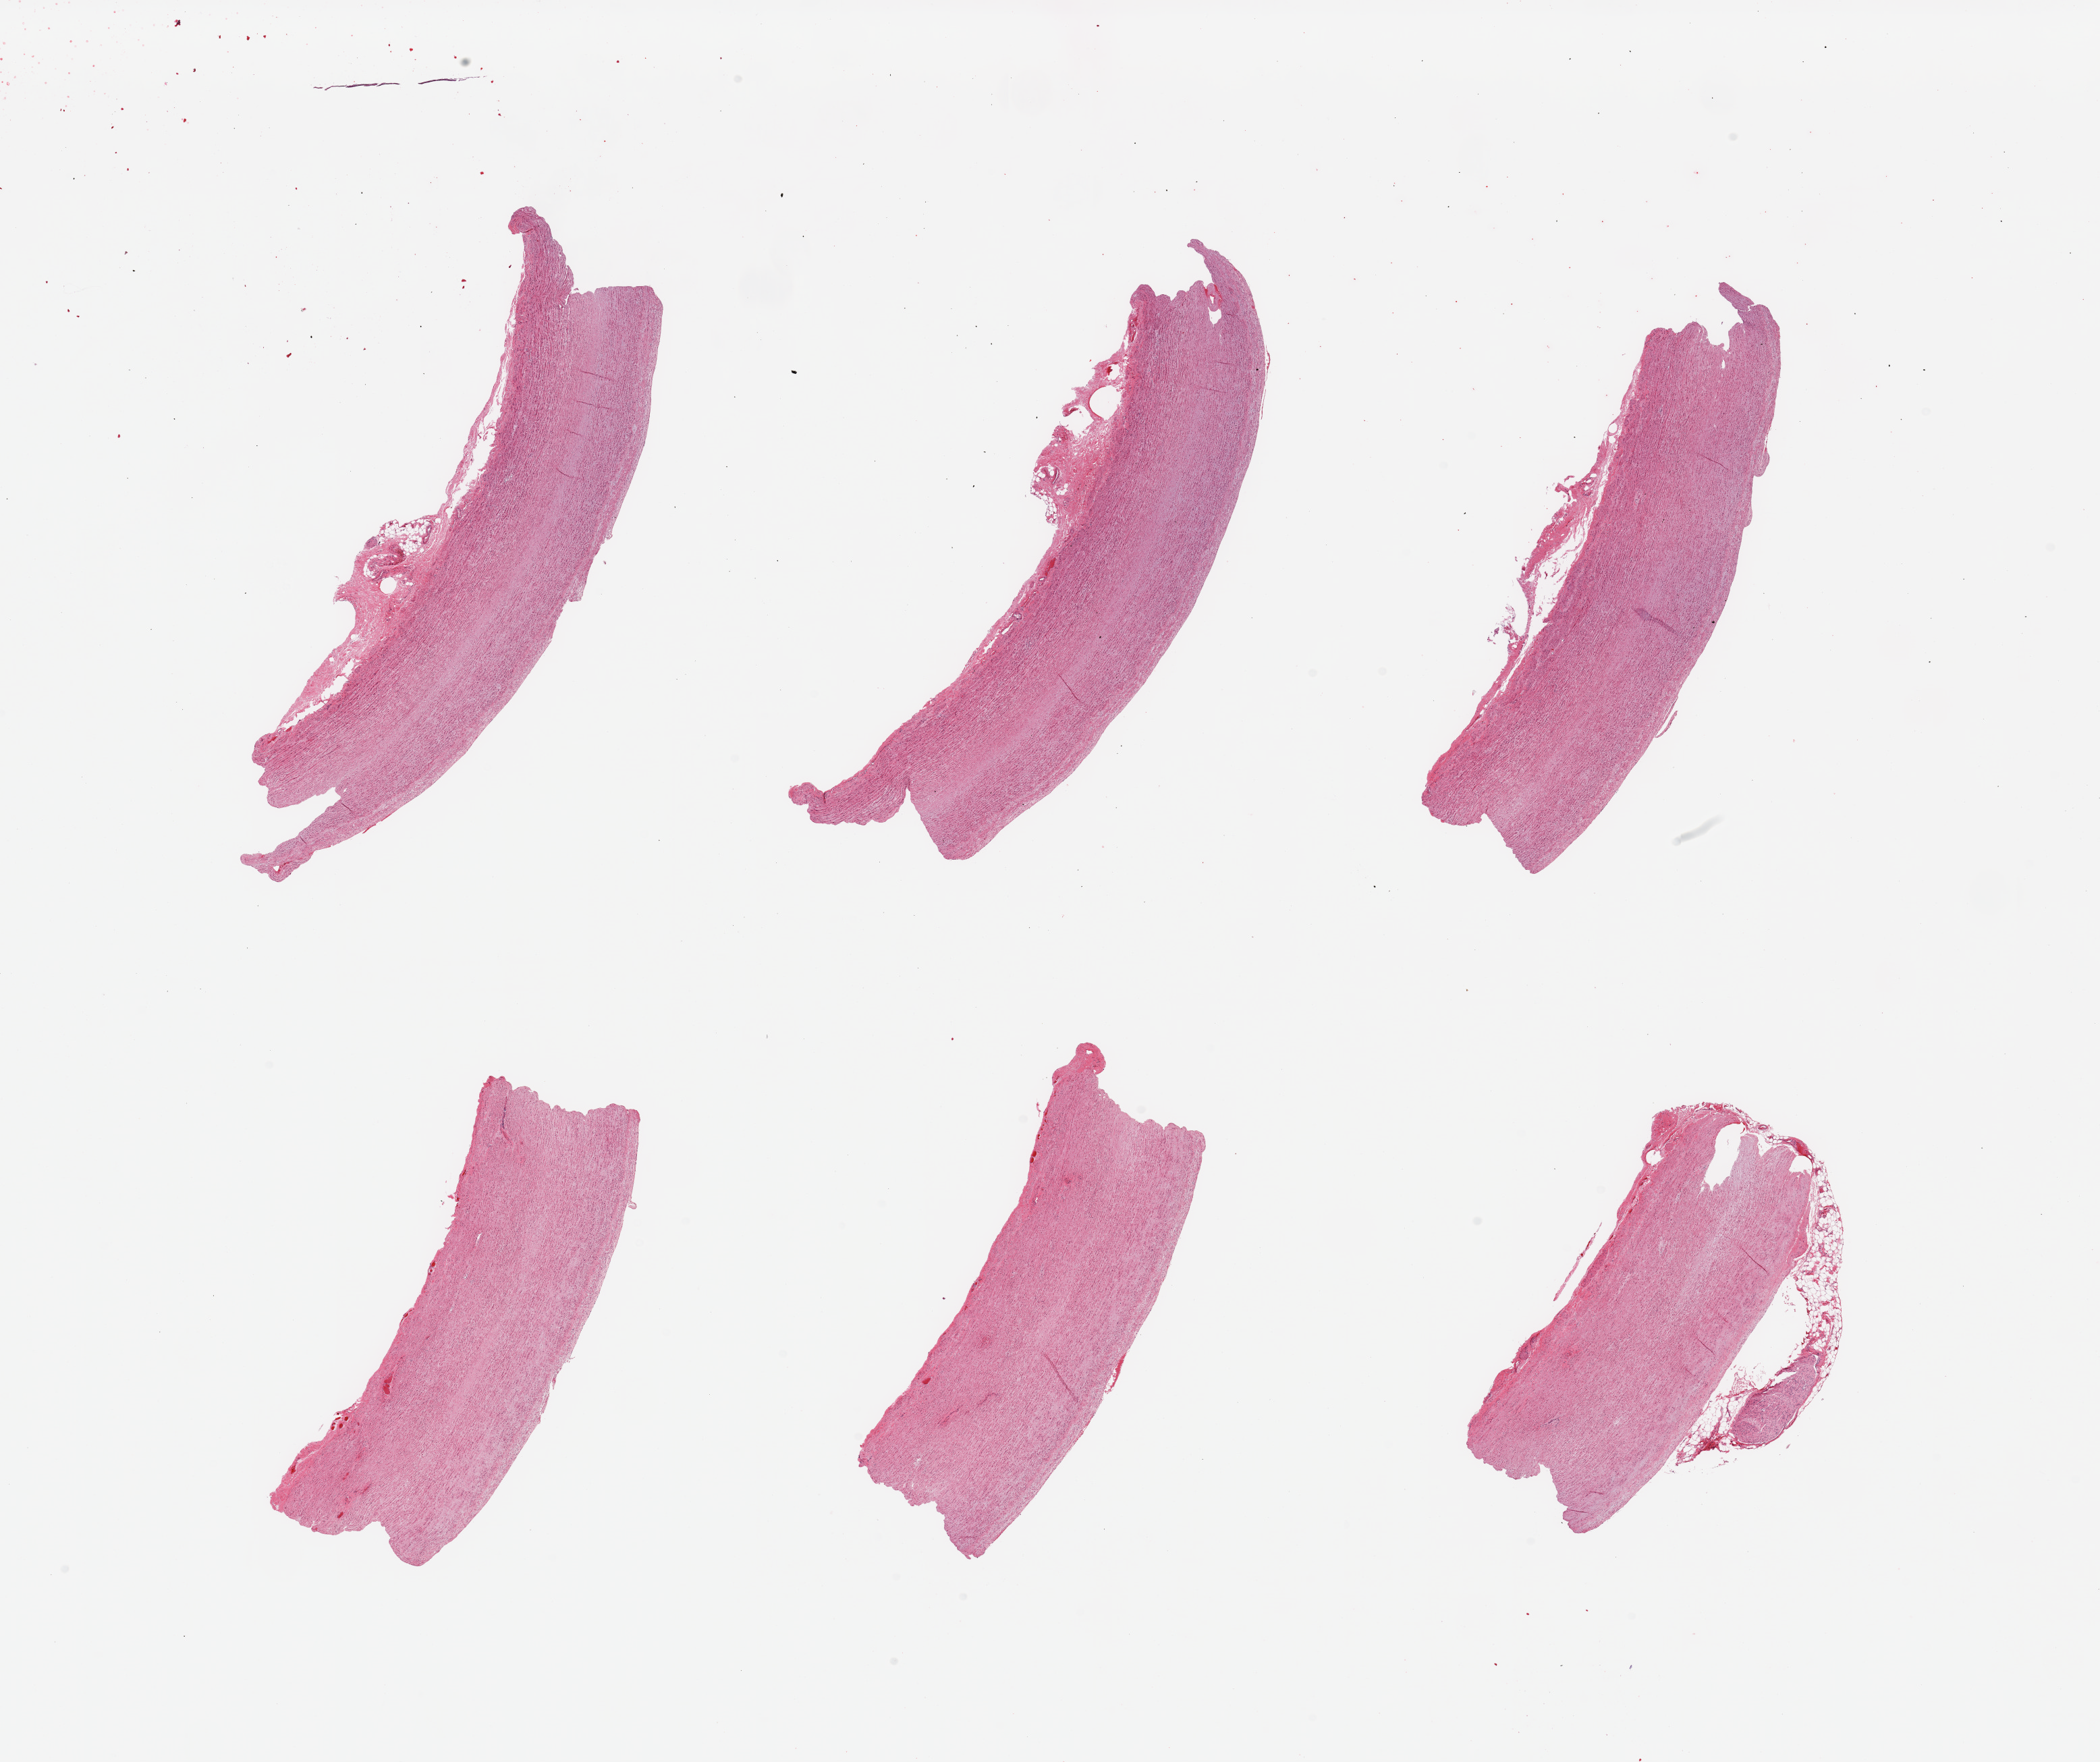
Whole-slide image, H&E stain — a low-resolution overview of the entire scanned area, about 24.6 x 20.6 mm (acquisition: 20x scan); PAXgene-fixed paraffin-embedded (PFPE) section; target tissue: aorta; tissue donor sample. Male donor.
Review note (as recorded): 6 pieces, minimal atherosis.